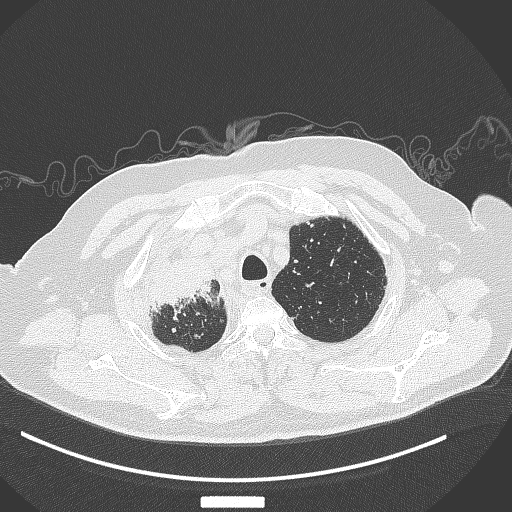
Chest CT, one axial slice; position 313 of 384 along the scan axis; reconstruction kernel B70f; 120 kVp; lung window (W 1500 / L -600 HU); 512 × 512 image matrix, field of view 400 × 400 mm. Male patient, age 69 years. From the clinical record (not read from this slice): clinical TNM (as recorded): T4 N3 M1.
Structures marked on this image (bounding box drawn by a radiologist):
- lung tumour (recorded histology: adenocarcinoma): bounding box <144,260,214,323> (left, top, right, bottom; pixels)